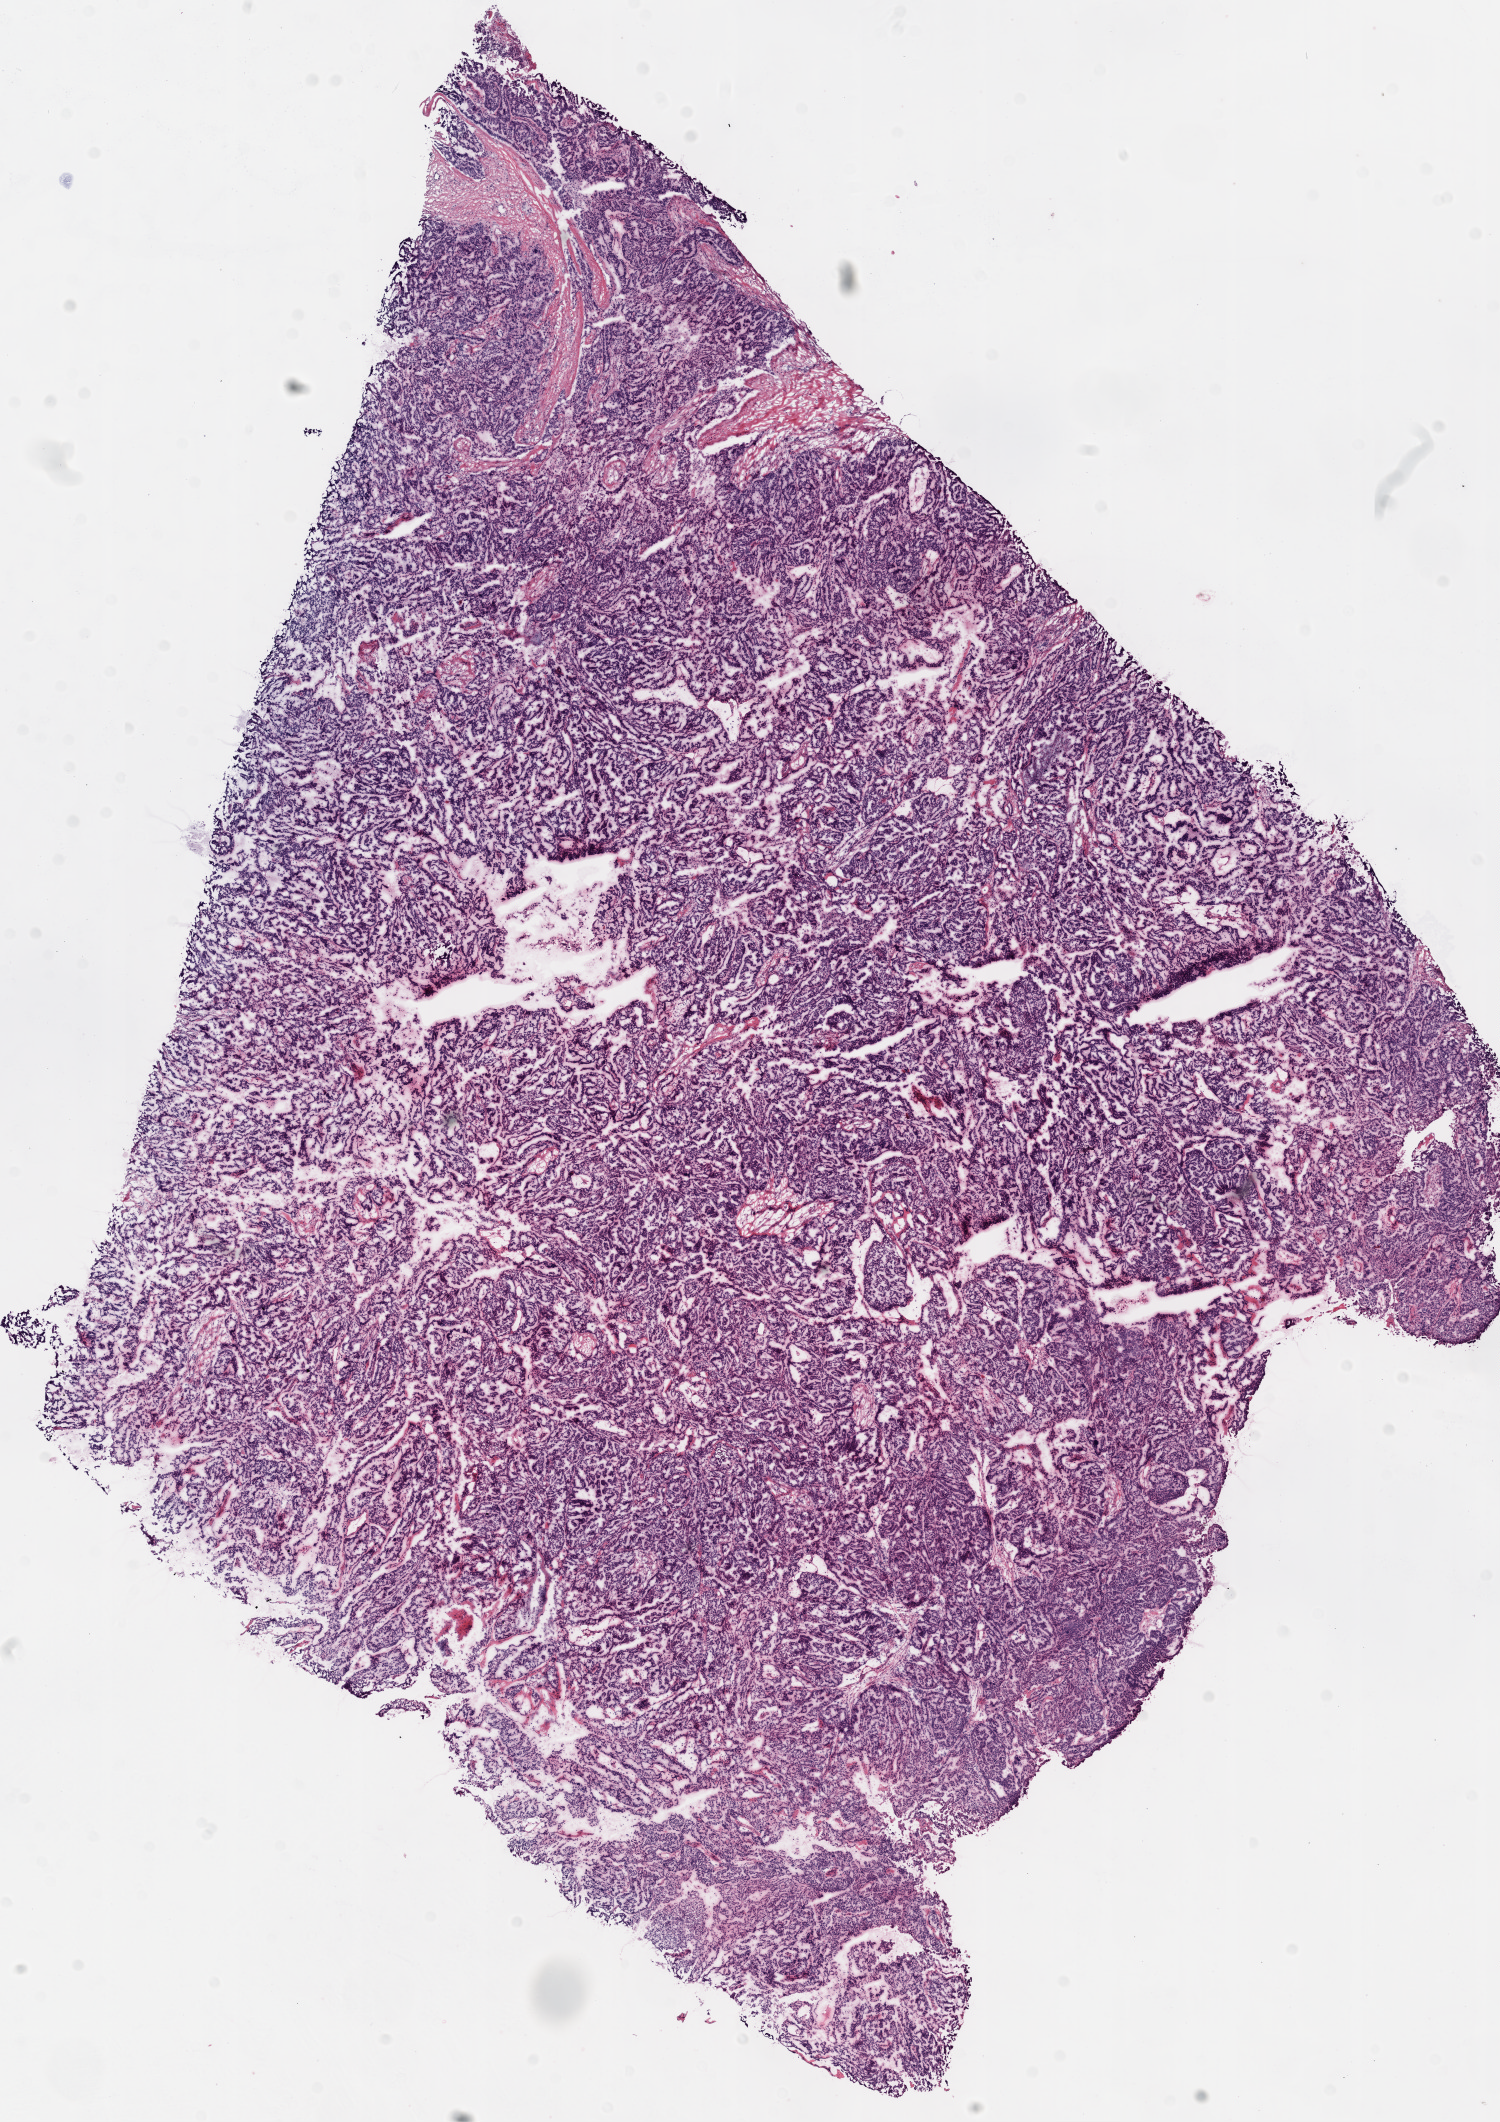
Digitized H&E-stained tissue section (whole slide), whole scanned area (about 12.0 x 17.0 mm) shown as a low-resolution overview; frozen section; primary tumour sample from the ovary. Female, age 51 years at initial diagnosis. Histologic grade: G3 (poorly differentiated). Composition of this section per pathologist review: tumour cells 94%, tumour nuclei 95%, normal cells 0%, stromal cells 5%, necrosis 1%.
• FIGO stage: IIIC
• histologic diagnosis: Serous cystadenocarcinoma, NOS